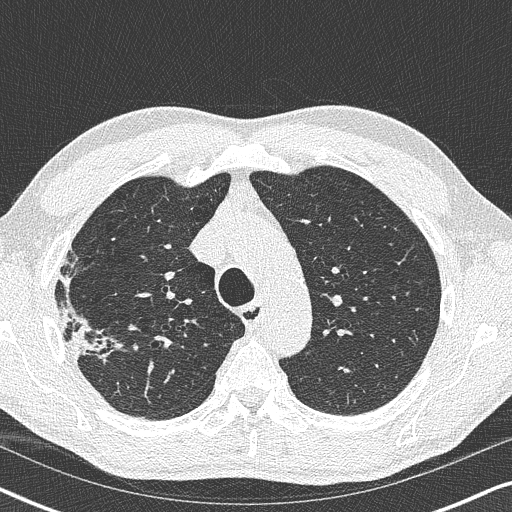
Low-dose screening chest CT, one axial slice; slice 272 of 356 in the series (ordered by position); 120 kVp; lung window (W 1500 / L -600 HU); 1 mm slice thickness; 512 × 512 image matrix, field of view 330 × 330 mm.
Structures marked on this image (outlined manually by an expert reader):
- lesion 1 (tumor, upper lobe of right lung): bounding box [x1, y1, x2, y2] px = [59, 301, 118, 358]